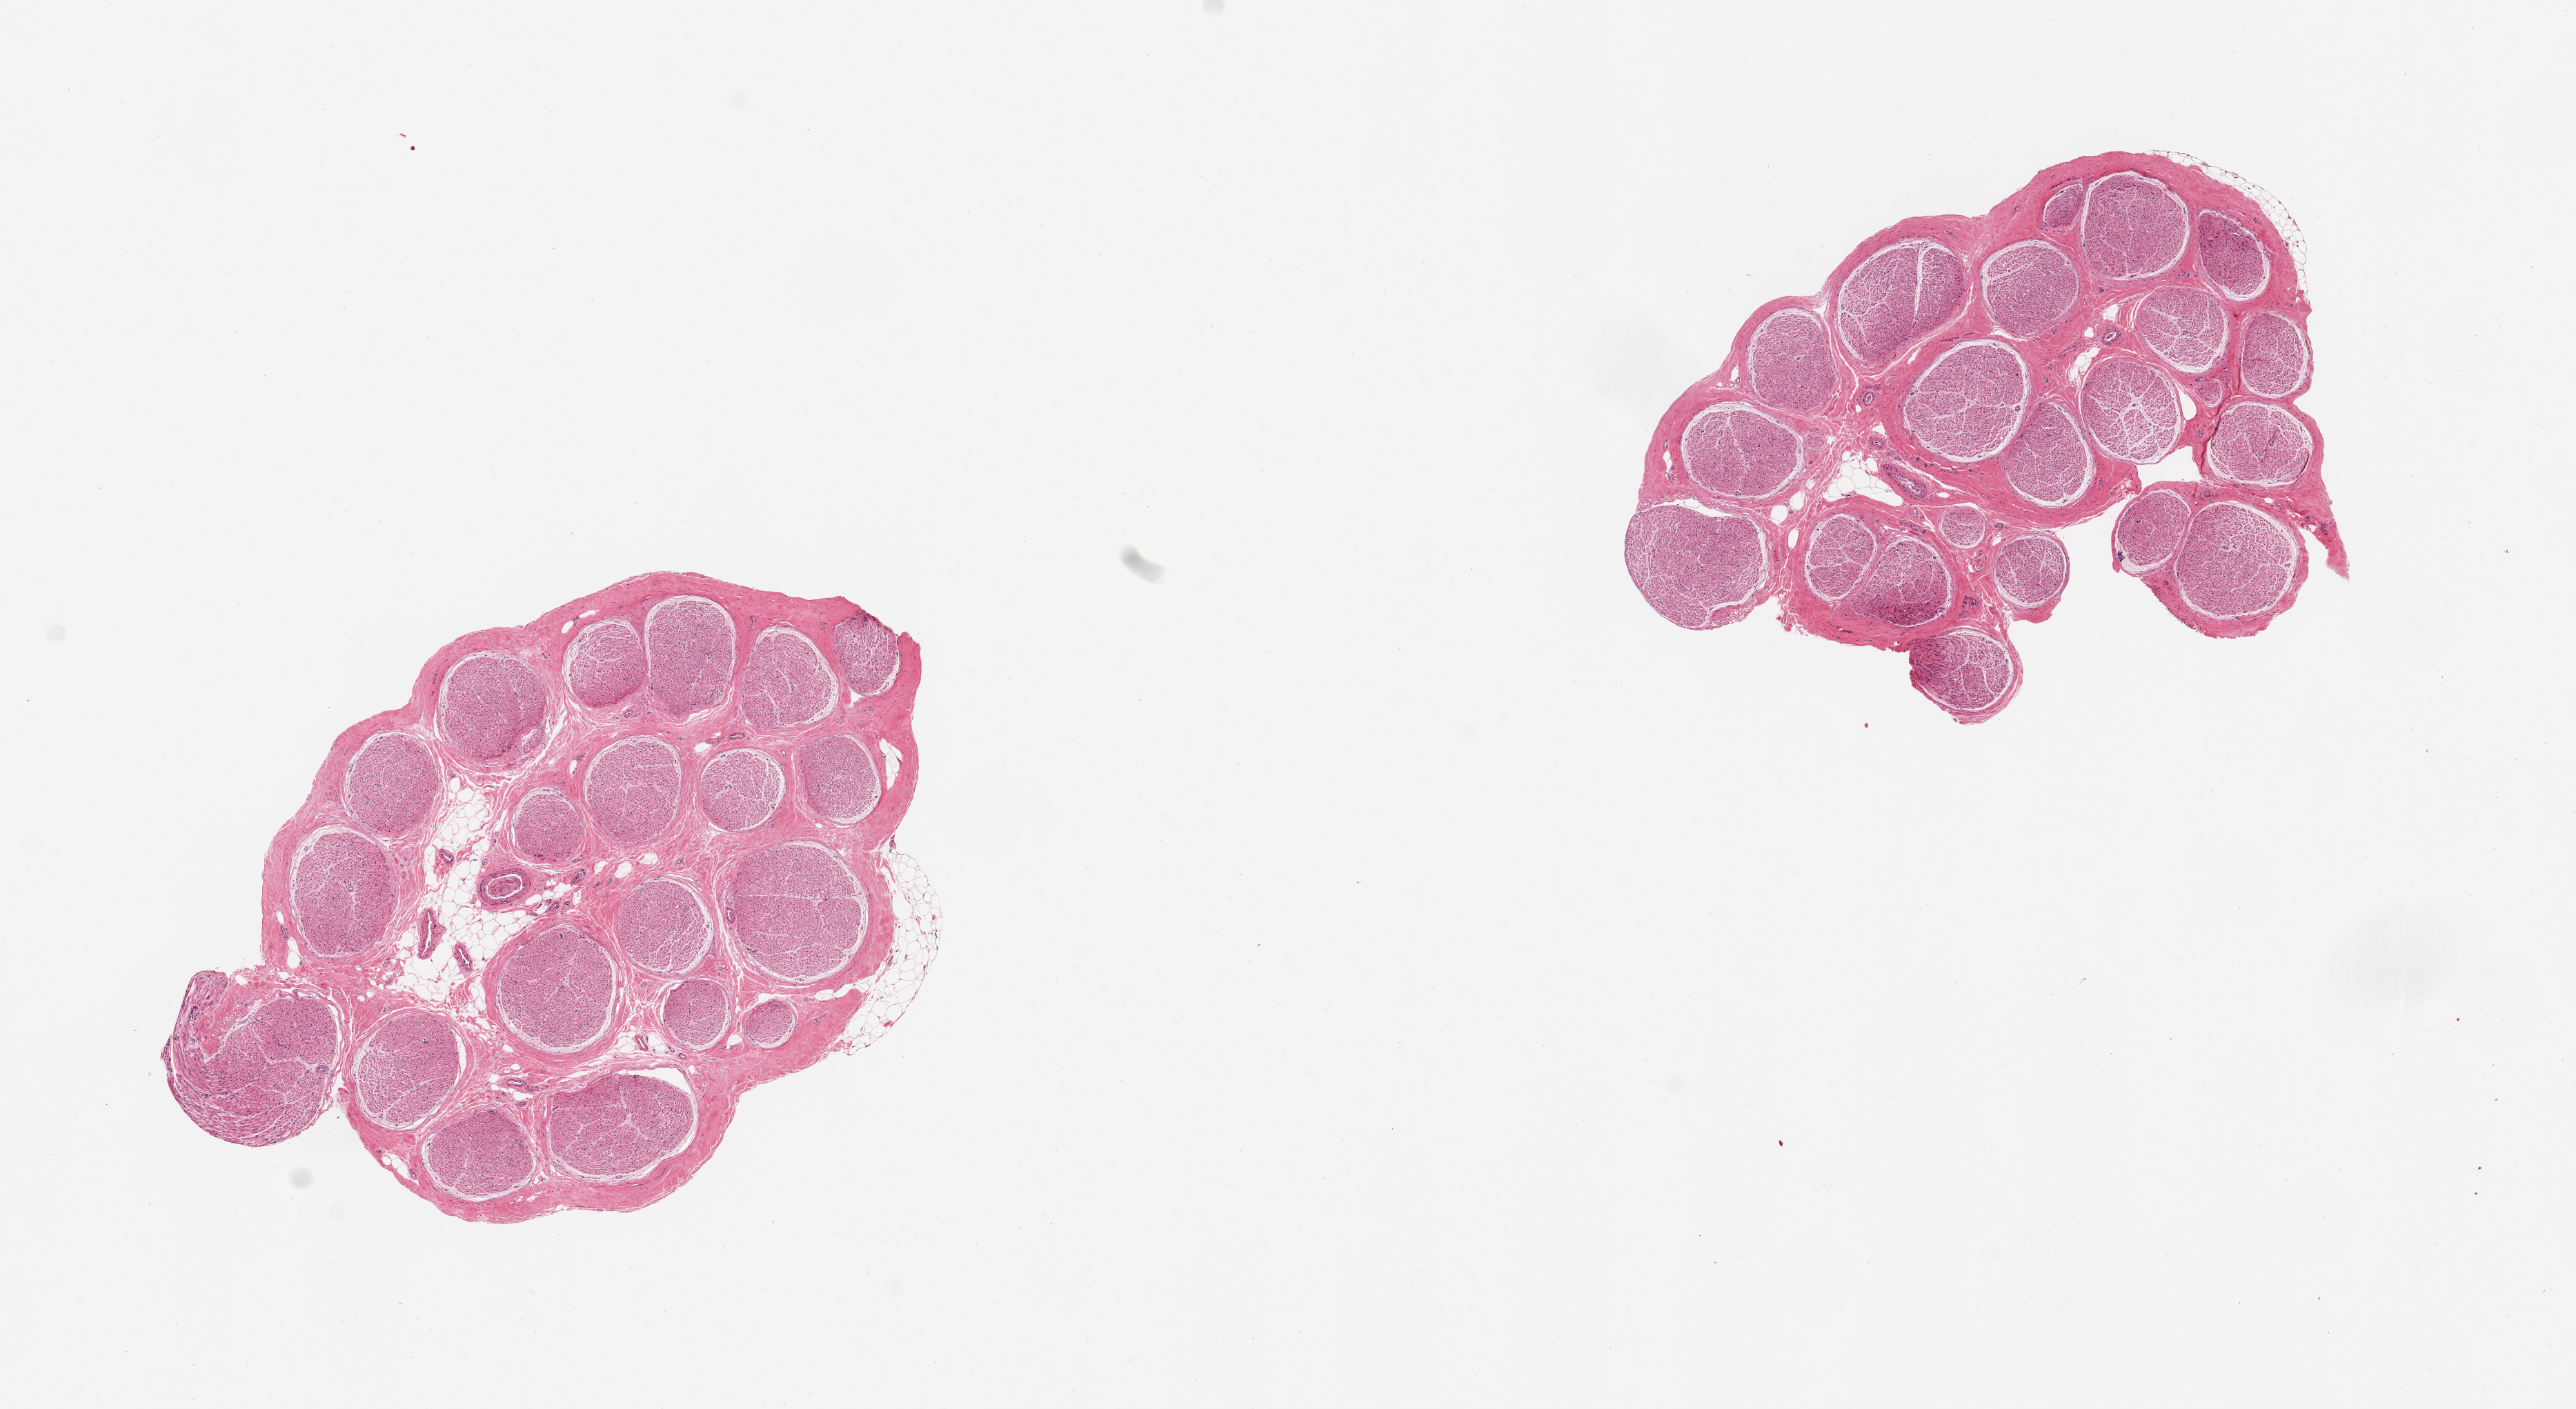
Whole-slide image, H&E stain, shown as a low-resolution overview of the whole scanned area (about 14.8 x 8.1 mm, acquisition: 20x scan); PAXgene-fixed, paraffin-embedded tissue; section of tibial nerve (target tissue); donor tissue sample. Donor: male.
Review note (as recorded): 2 pieces; 5 & 10% internal fat.